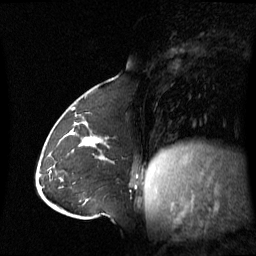
Breast MRI (dynamic contrast-enhanced), one sagittal slice. Slice 24 of 60 in the series (ordered by position). Dynamic contrast-enhanced series, image 2 of 3 at this slice position (ordered by acquisition). 1.5 T. TE 4.2 ms, TR 8.4 ms. 2.8 mm slice thickness. 256 × 256 image matrix. Female patient, age 43 years. From the clinical record (not read from this slice): setting: breast cancer imaged before/during neoadjuvant chemotherapy; receptor status: triple-negative.
Structures marked on this image (semi-automatic segmentation, software-assisted and operator-edited):
- analysis volume of interest (the breast-tissue region the enhancement analysis was run in; not a lesion): bounding box (x1, y1, x2, y2) in pixels: (62, 124, 137, 180)
- tumour enhancement mask (voxels above the 70 % enhancement threshold inside the analysis volume of interest): (69, 124, 101, 146)